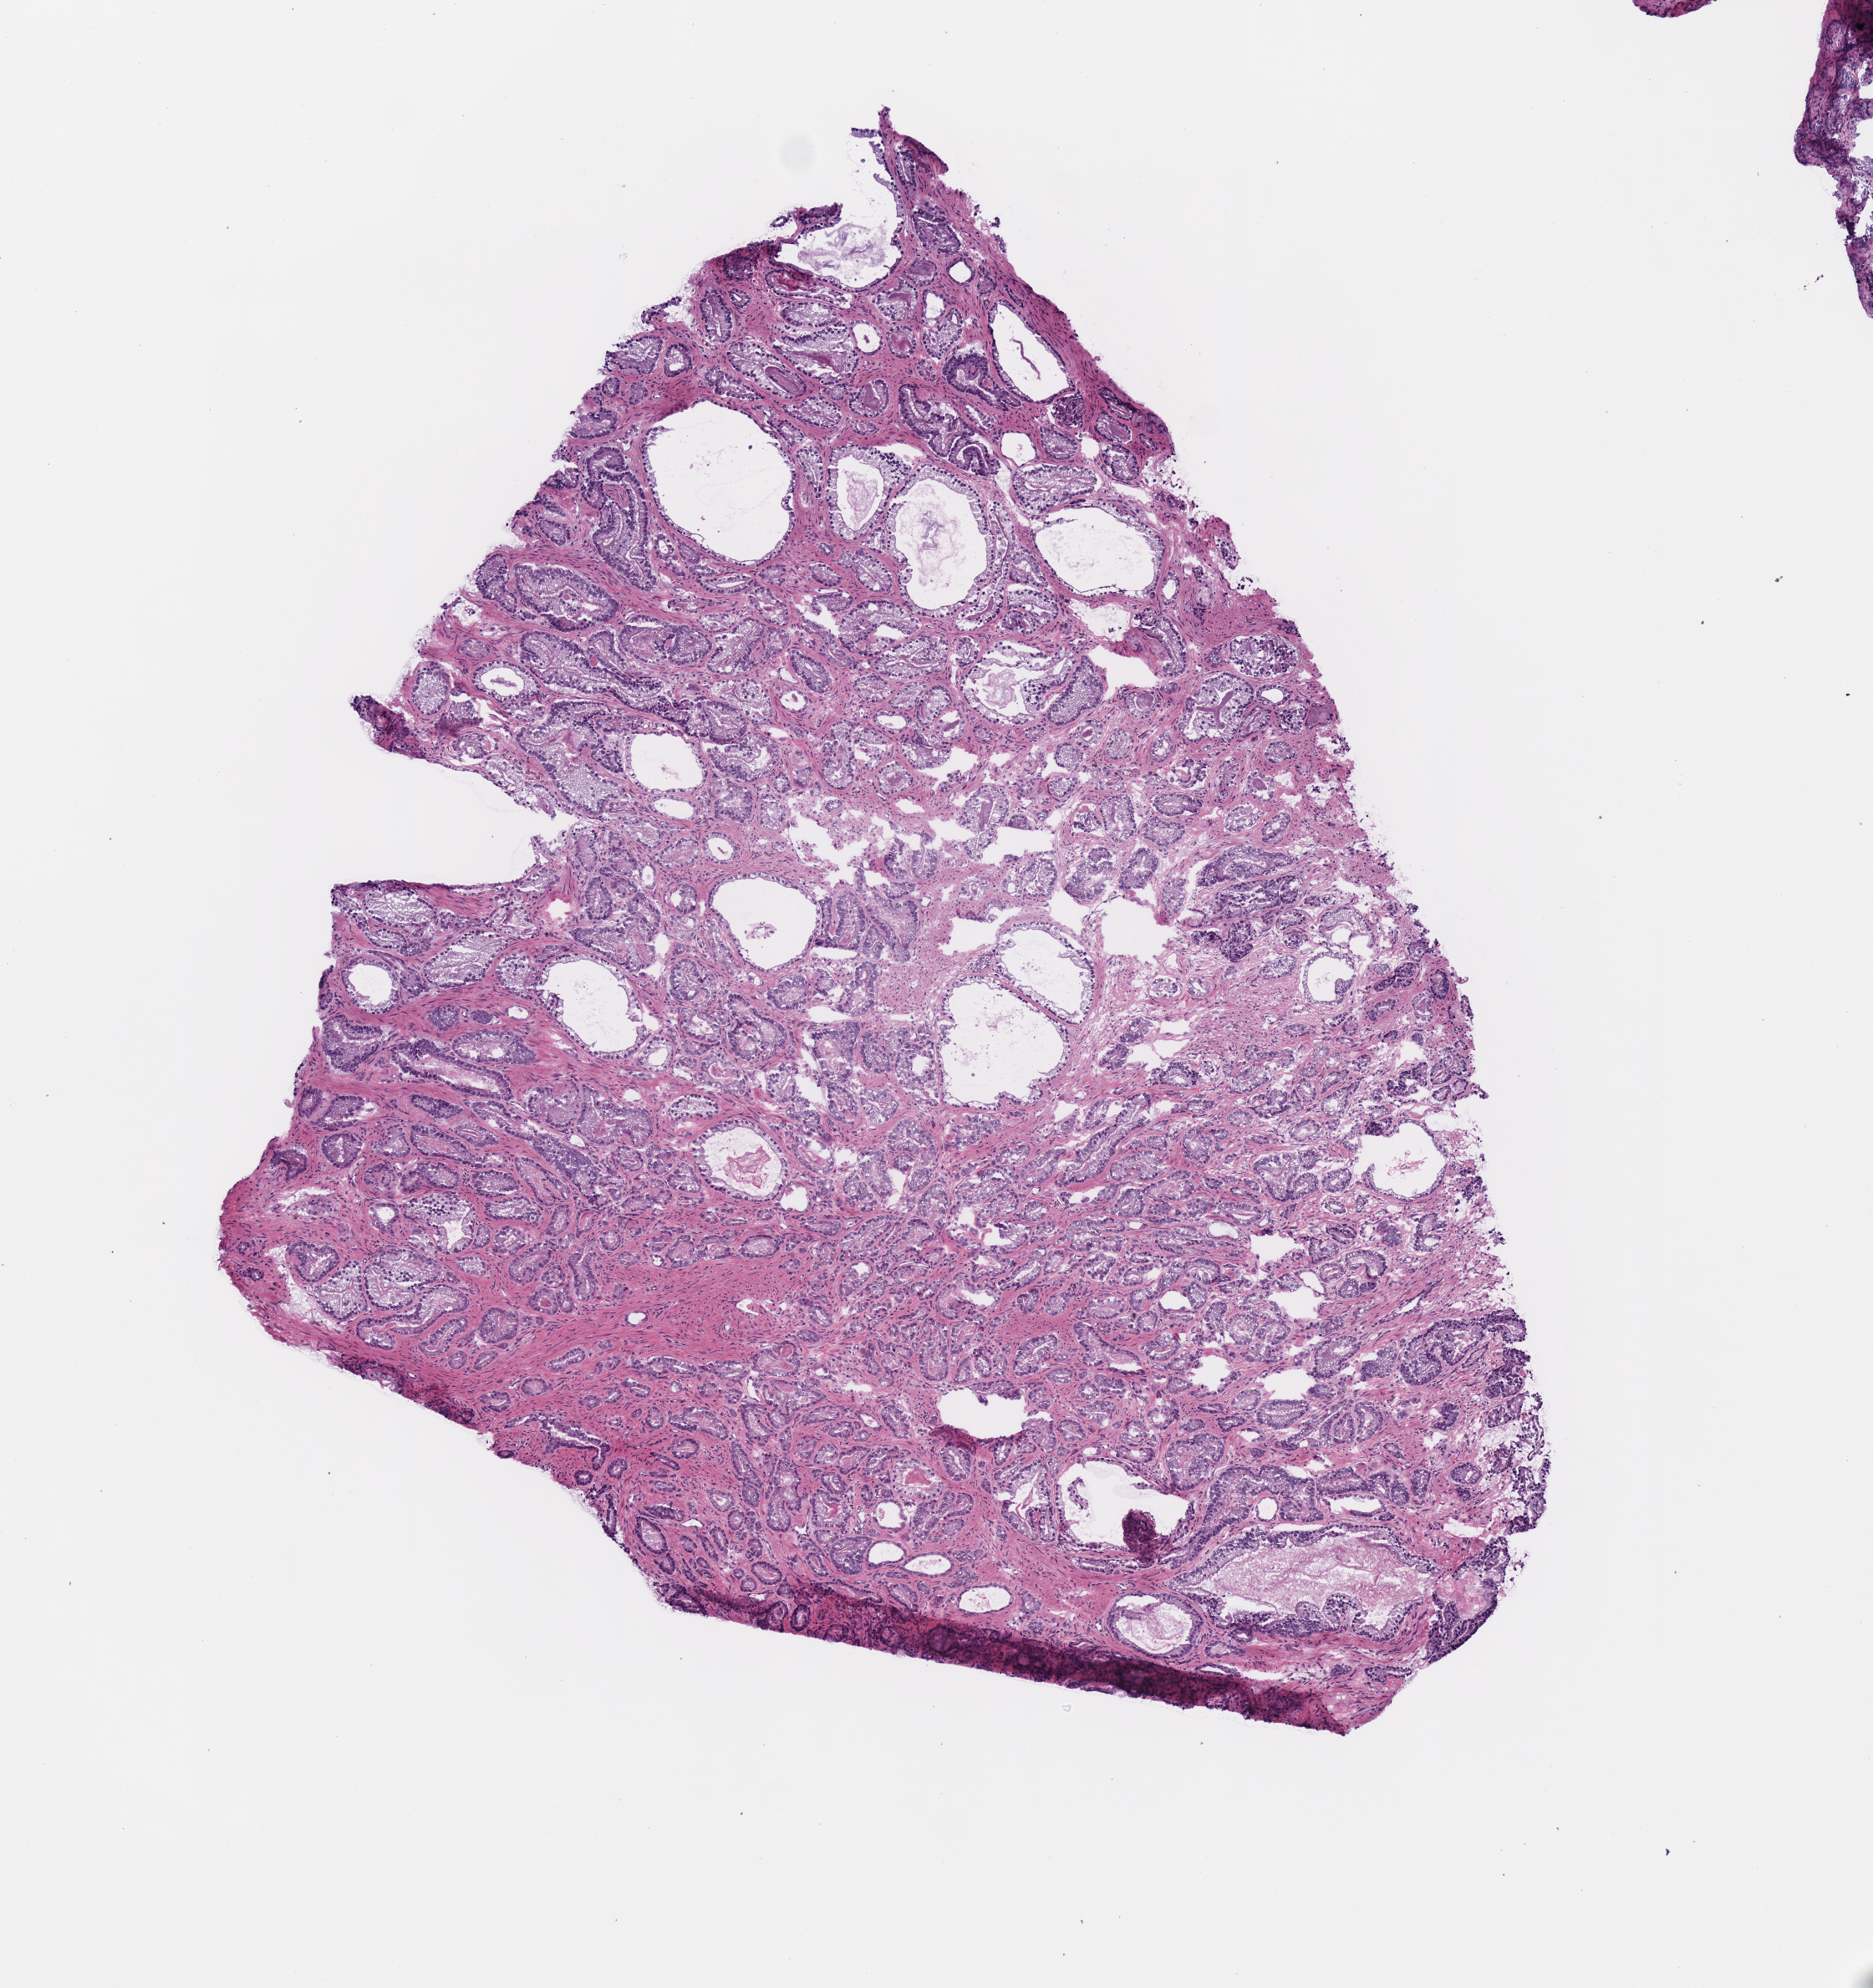
H&E whole-slide image — low-resolution overview of the scanned area, about 4.4 x 4.7 mm (slide scanned at 40x); frozen section; primary tumour sample from the prostate. Male patient; age at initial diagnosis 68 years. Slide review estimates, as recorded: tumour cells 75%, tumour nuclei 75%.
Histologic diagnosis: Acinar cell carcinoma (prostate gland).